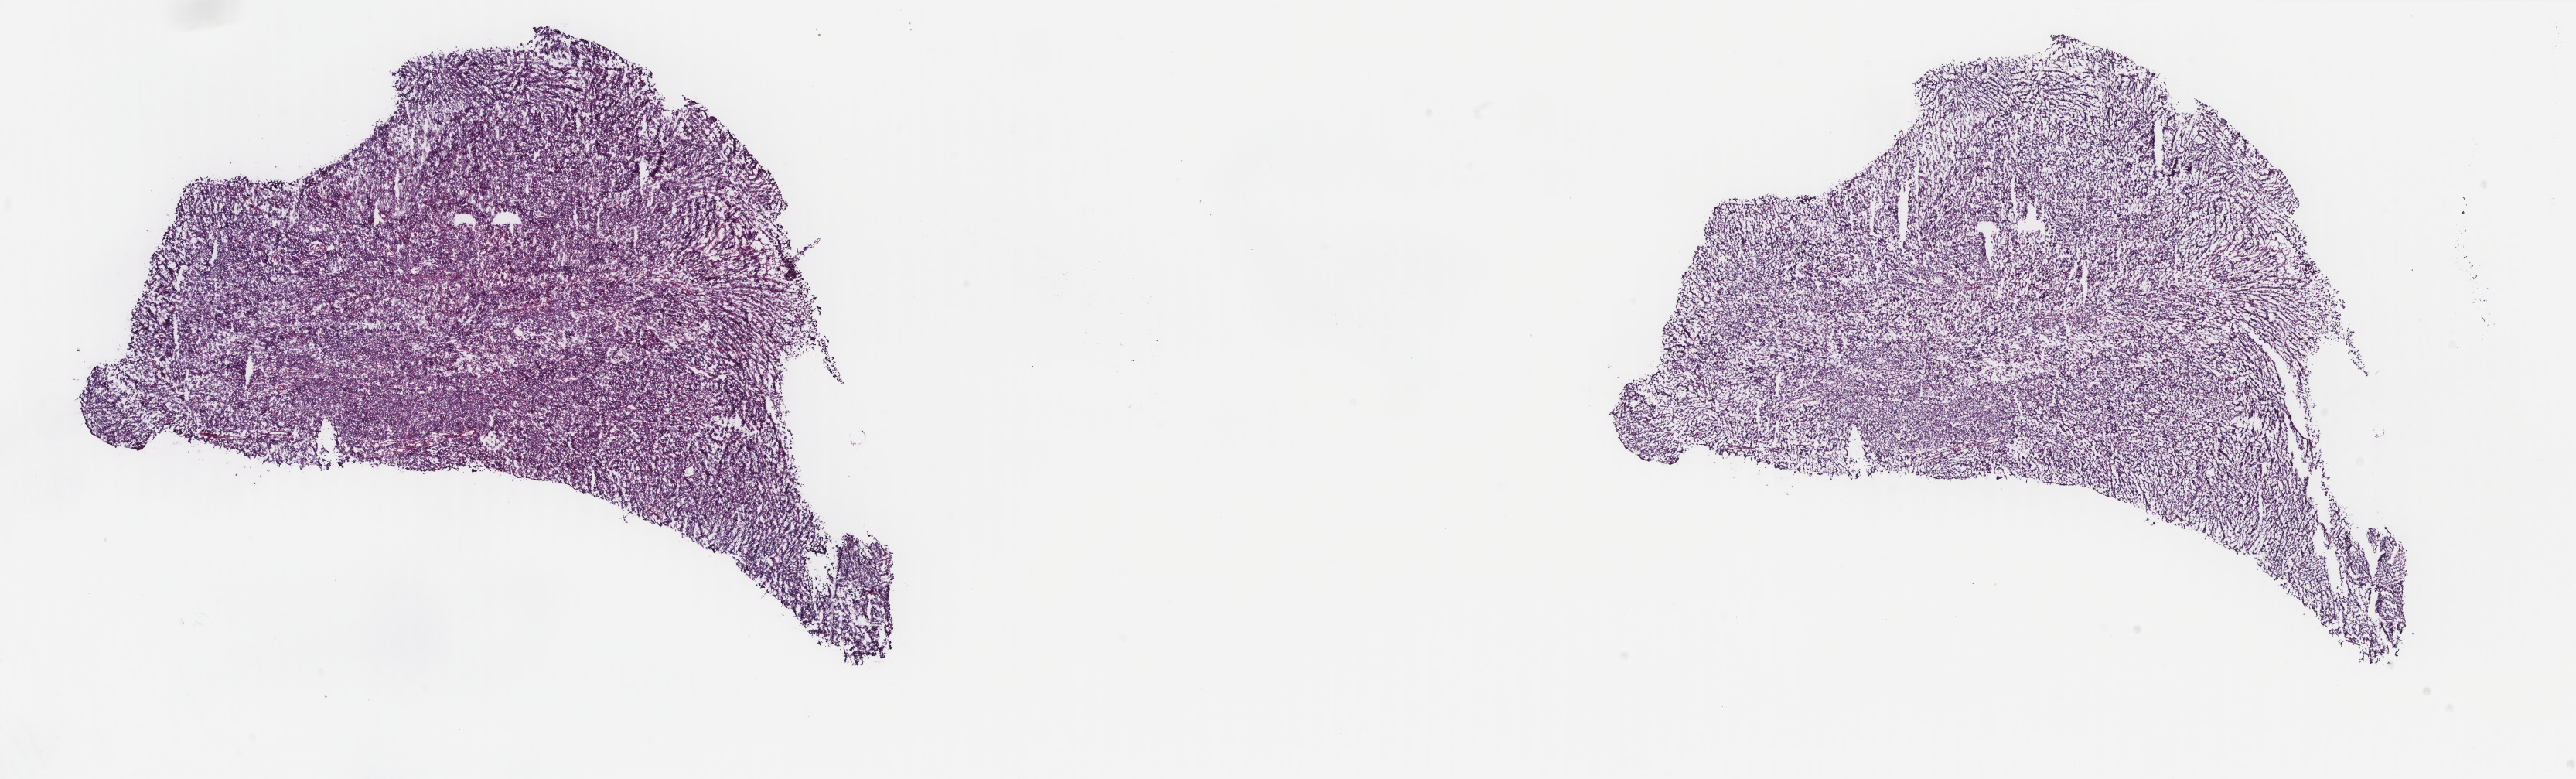
Hematoxylin and eosin (H&E) stained whole-slide image, shown as a low-resolution overview of the whole scanned area (about 26.4 x 8.0 mm, from a 40x scan). Frozen section. Primary tumour sample from the uterus. Patient: female, age at initial diagnosis 72 years. Histologic grade: G3 (poorly differentiated). Slide review estimates, as recorded: tumour cells 90%, tumour nuclei 90%, normal cells 0%, stromal cells 5%, necrosis 5%. Infiltration values recorded for this section: lymphocyte infiltration 60%, monocyte infiltration 20%, neutrophil infiltration 10%.
• FIGO stage: IB
• diagnosis: Serous cystadenocarcinoma, NOS (endometrium)